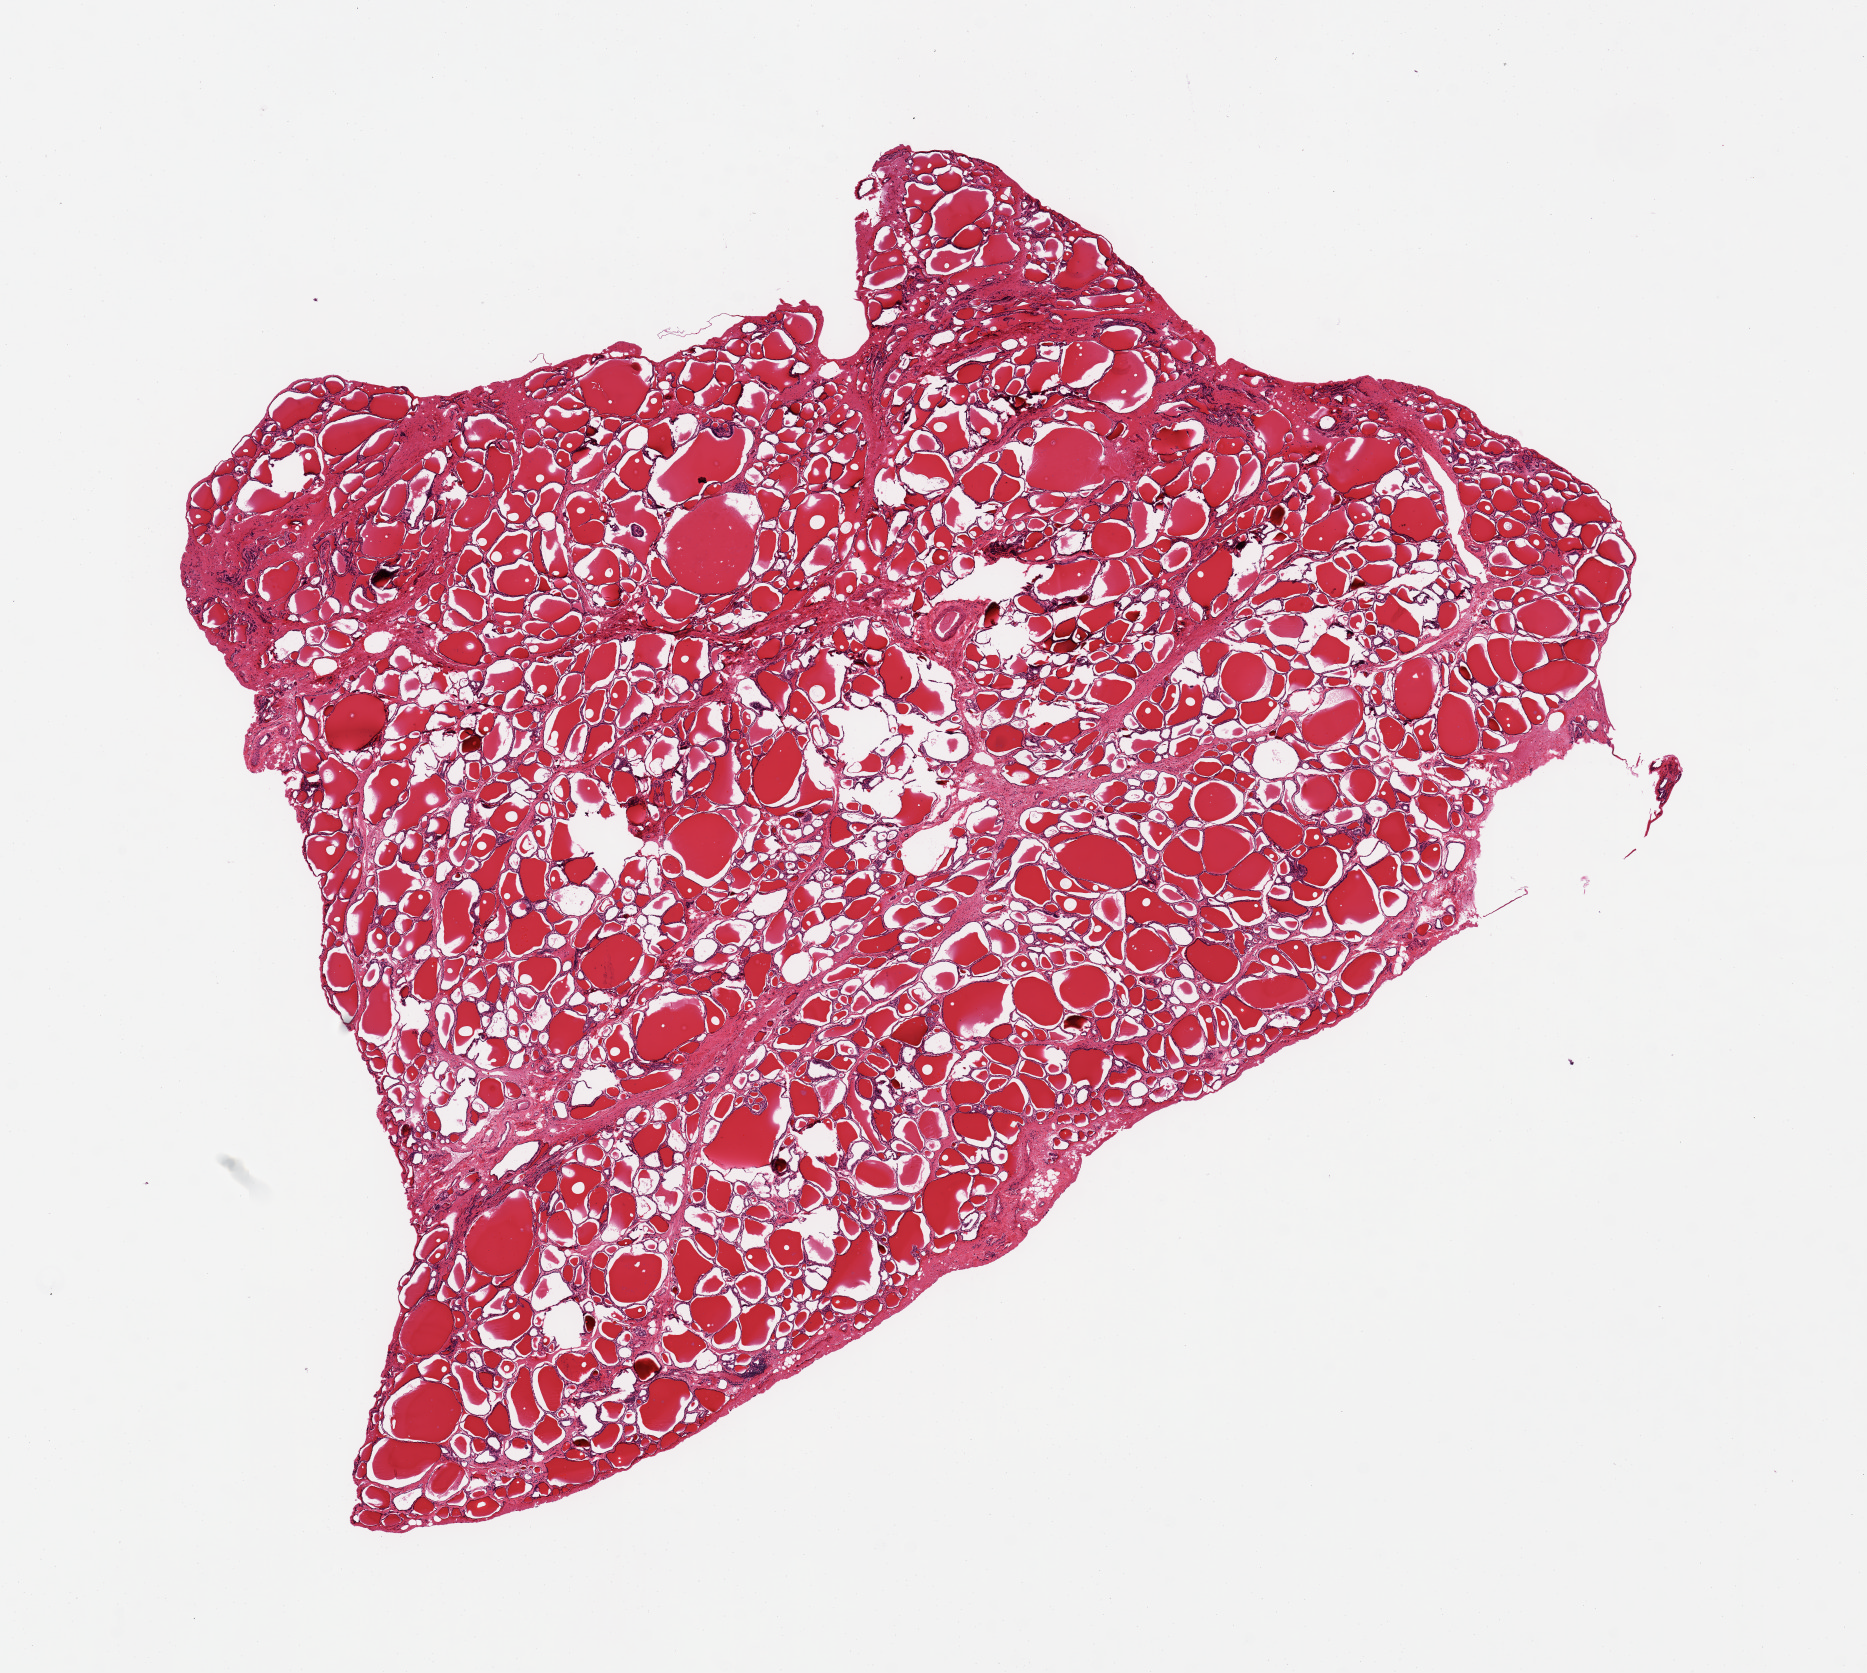
Digitized haematoxylin and eosin-stained section, whole scanned area (about 14.8 x 13.2 mm, from a 20x scan) shown as a low-resolution overview. PAXgene-fixed, paraffin-embedded tissue. Sampled site (target tissue): thyroid. Donor tissue sample.
- pathologist's review note for this sample: 10.5 x 11.5 mm specimen, no adenomatoid nodules noted